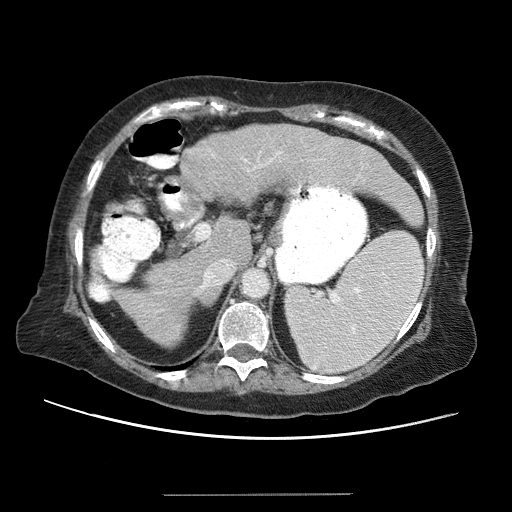
Contrast-enhanced abdominal CT (liver protocol), one axial slice; position 37 of 65 along the scan axis; 120 kVp; soft-tissue window (W 400 / L 40 HU); 512 × 512 image matrix. Case-level facts recorded for this patient, not image findings: diagnosis: hepatocellular carcinoma (patient treated with transarterial chemoembolisation; whether this scan precedes or follows treatment is not stated here); TNM stage (as recorded): Stage-IIIB; Child-Pugh class: A.
Annotated regions visible in this slice (semi-automatically segmented with operator editing):
- liver parenchyma outside the tumour (the mass and vessels are separate outlines, so this box may not span the whole liver): bounding box (x1, y1, x2, y2) in pixels: (88, 124, 406, 348)
- liver vessels: (94, 145, 374, 336)